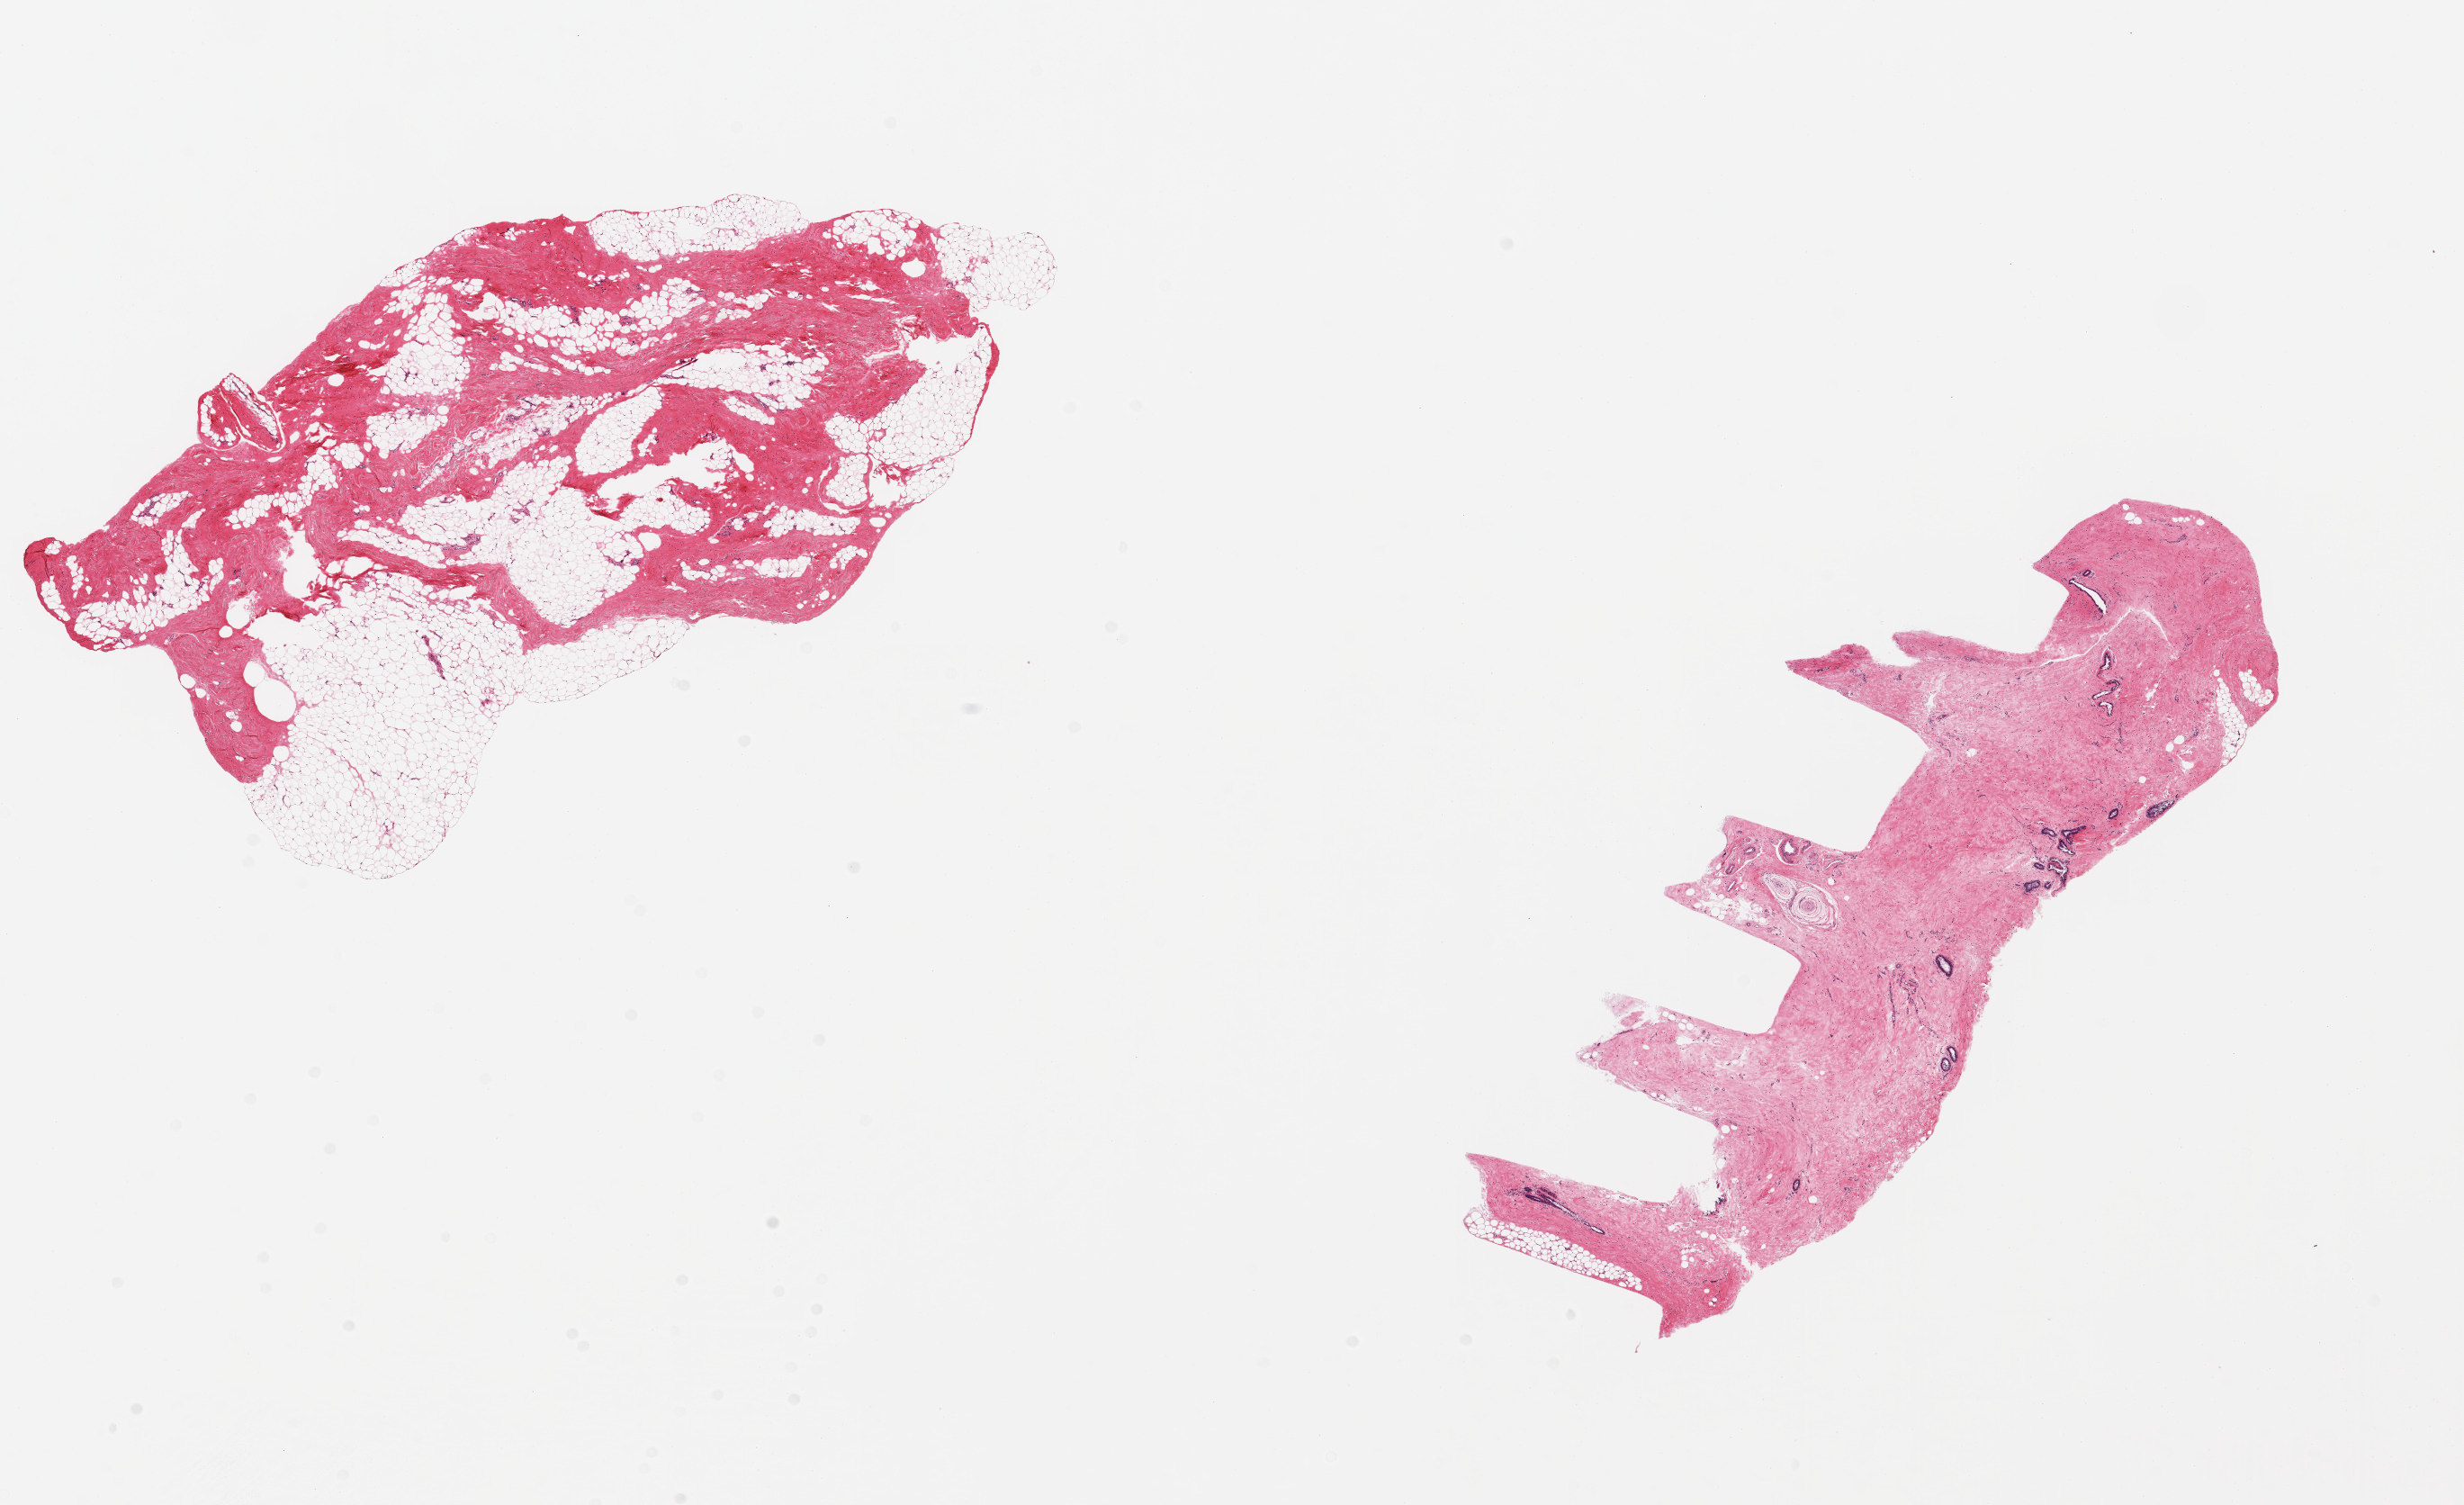
Digitized haematoxylin and eosin-stained section — low-resolution overview of the scanned area, about 21.7 x 13.2 mm. PAXgene-fixed paraffin-embedded (PFPE) section. Section of breast (target tissue). Donor tissue sample. Donor: male.
Pathologist's review note for this sample: 2 pieces, 8x4 & 9x4mm; 1 fibroadipose; 1 gynecomastia with fibrosis and ducts.